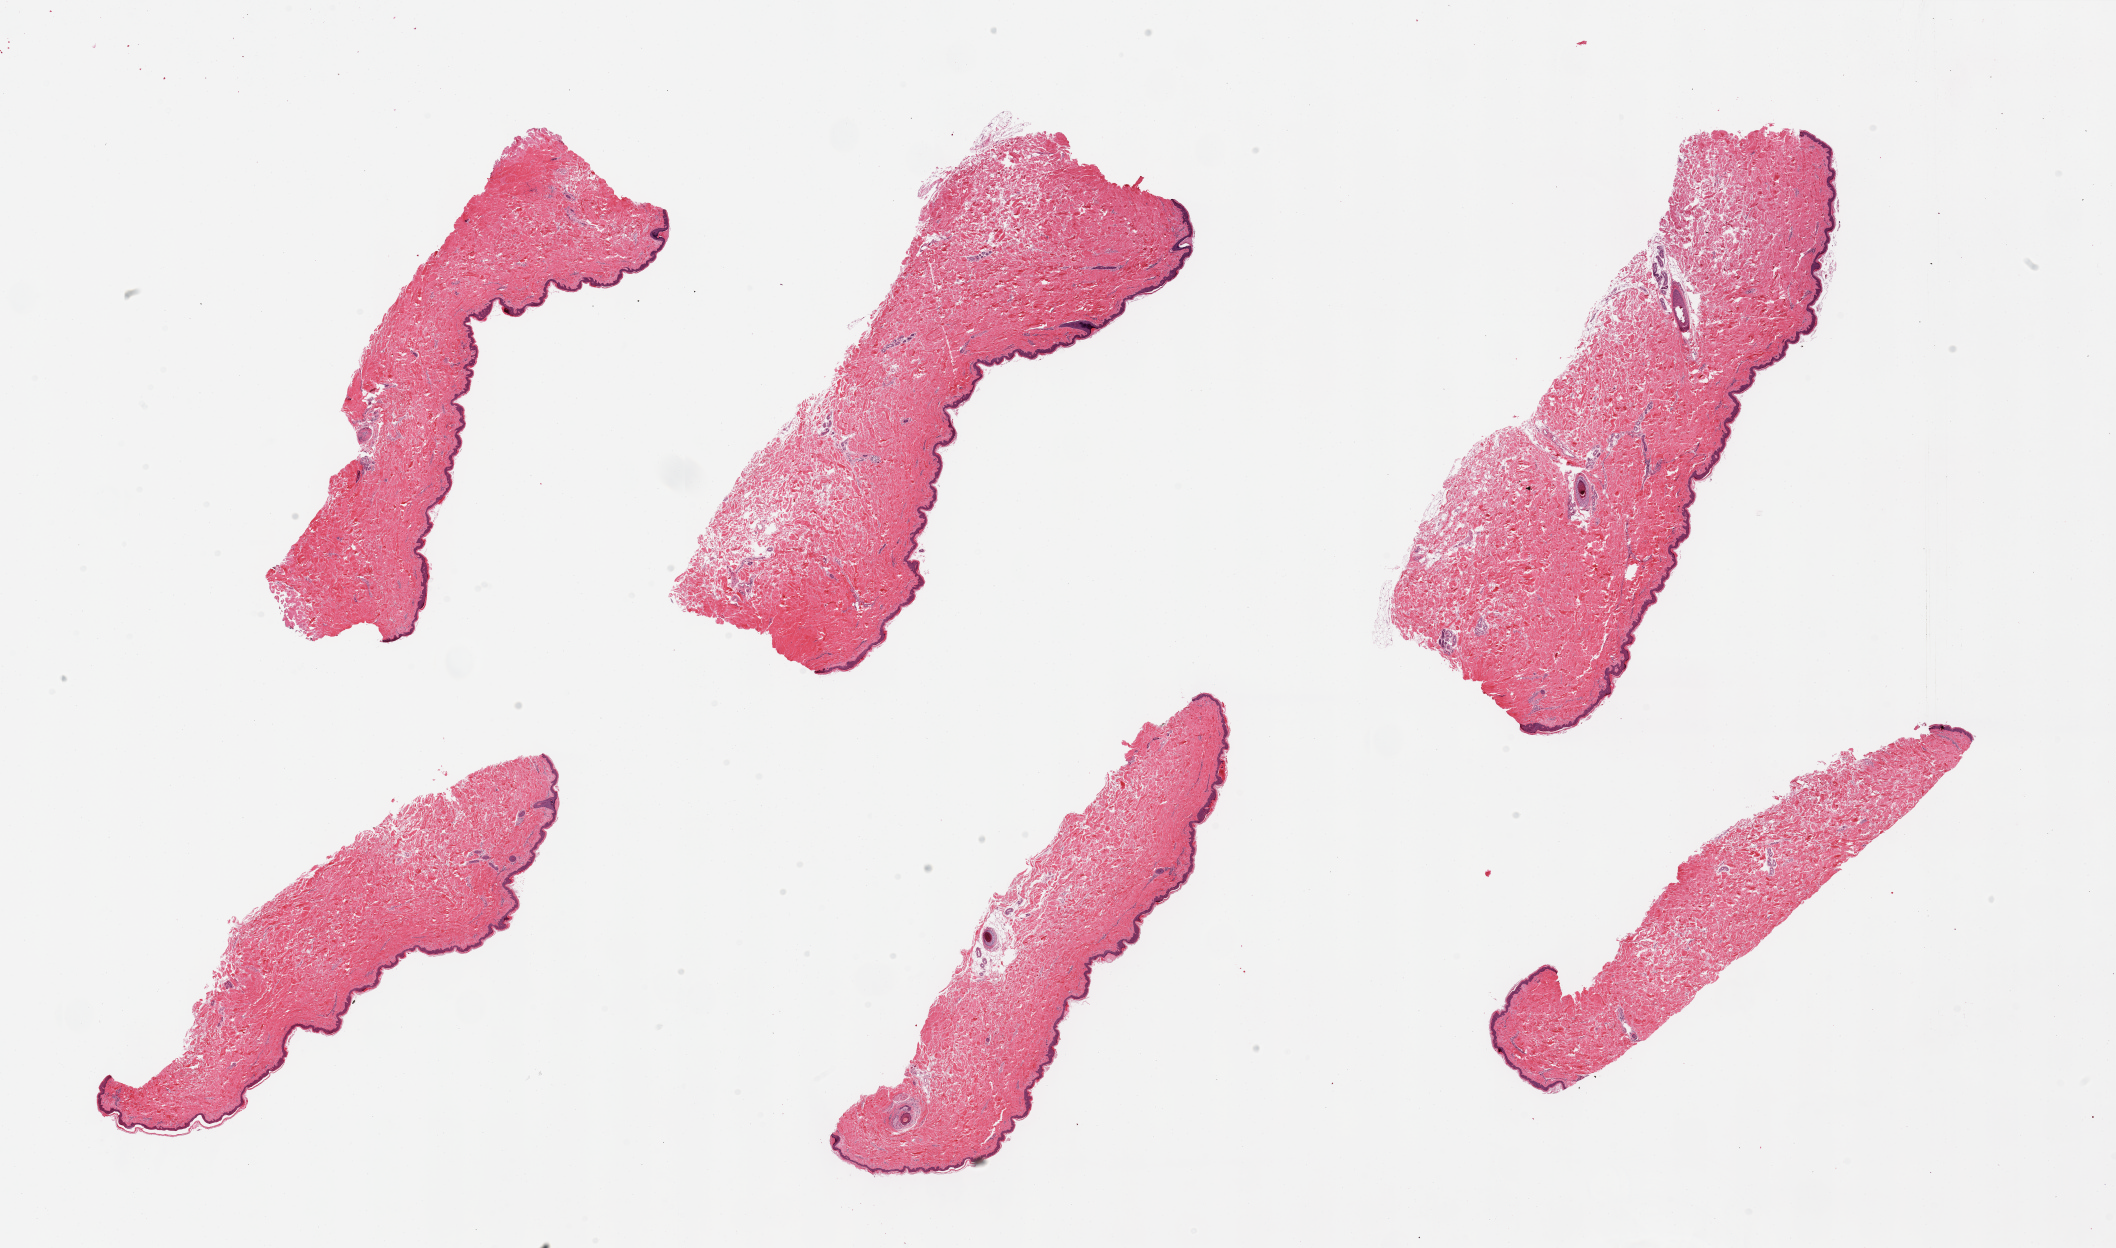
Haematoxylin and eosin whole-slide image, shown as a low-resolution overview of the whole scanned area (about 33.5 x 19.7 mm, slide scanned at 20x); PAXgene-fixed, paraffin-embedded tissue; target tissue: skin of suprapubic region; tissue donor sample.
Pathologist's review note for this sample: 6 pieces; well trimmed.